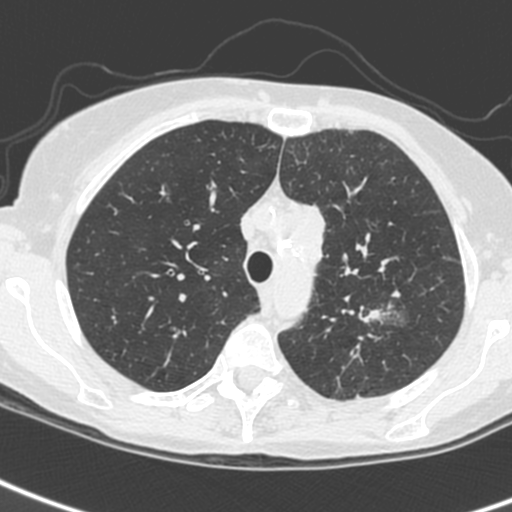
Low-dose screening chest CT, one axial slice. Slice 190 of 242 in the series (ordered by position). 120 kVp. Lung window (W 1500 / L -600 HU). 1.3 mm slice thickness. 512 × 512 image matrix, field of view 284 × 284 mm.
Annotated regions visible in this slice (manually delineated by an expert):
- lesion 3 (tumor, upper lobe of left lung): bounding box [x1, y1, x2, y2] px = [298, 204, 326, 267]